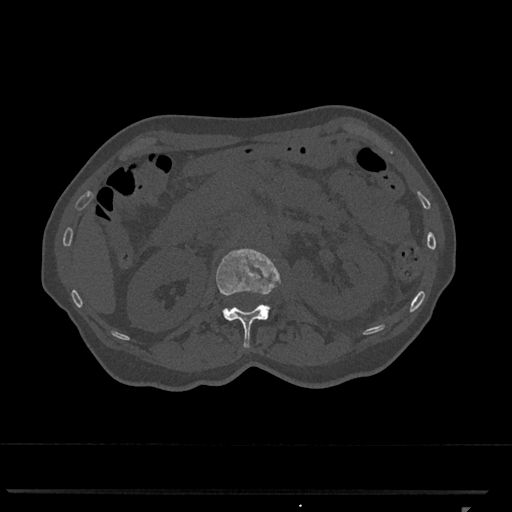
CT including the spine, one axial slice. Reconstruction kernel Br40s/3. 120 kVp. Bone window (W 1800 / L 400 HU). 512 × 512 image matrix. Patient: female, 62 years. Case-level facts recorded for this patient, not image findings: primary cancer: renal.
Structures marked on this image (semi-automatic segmentation, software-assisted and operator-edited):
- L1 vertebra: bounding box (x1, y1, x2, y2) in pixels: (216, 248, 281, 348)